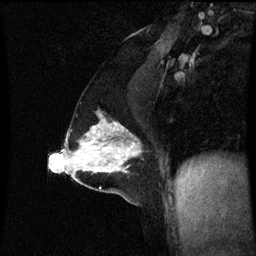
Breast MRI (dynamic contrast-enhanced), one sagittal slice; slice 36 of 60 in the series (ordered by position); dynamic contrast-enhanced series, image 2 of 3 at this slice position (ordered by acquisition); 1.5 T; TE 4.2 ms, TR 8.9 ms; 2.1 mm slice thickness; 256 × 256 image matrix. Patient: female, 47 years. Case-level facts recorded for this patient, not image findings: setting: breast cancer imaged before/during neoadjuvant chemotherapy; receptor status: HR-positive, HER2-negative.
Outlined on this slice (semi-automatic segmentation, software-assisted and operator-edited):
- analysis volume of interest (the breast-tissue region the enhancement analysis was run in; not a lesion): box from (x=71, y=116) to (x=143, y=163) px
- tumour enhancement mask (voxels above the 70 % enhancement threshold inside the analysis volume of interest): (x=94, y=120)–(x=140, y=155)